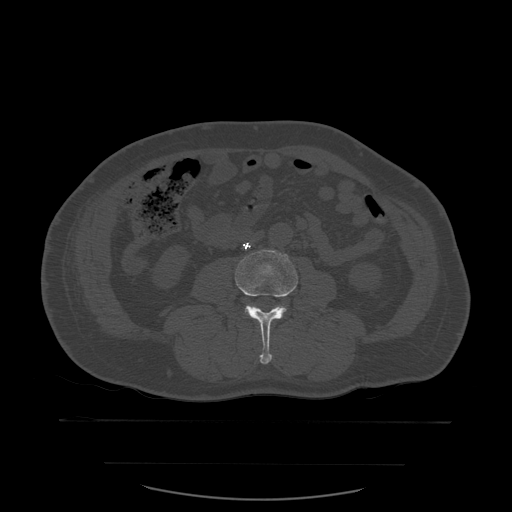
CT including the spine, one axial slice. Slice 188 of 590 in the series (ordered by position). Bone window (W 1800 / L 400 HU). 512 × 512 image matrix, field of view 479 × 479 mm. Patient age 71 years. Case-level facts recorded for this patient, not image findings: primary cancer: lung; vertebrae with lytic lesions (as recorded): T1, T2, L5, S1.
Structures marked on this image (semi-automatic segmentation, software-assisted and operator-edited):
- L3 vertebra: box from (x=235, y=250) to (x=298, y=365) px
- L4 vertebra: (x=246, y=310)–(x=250, y=315)